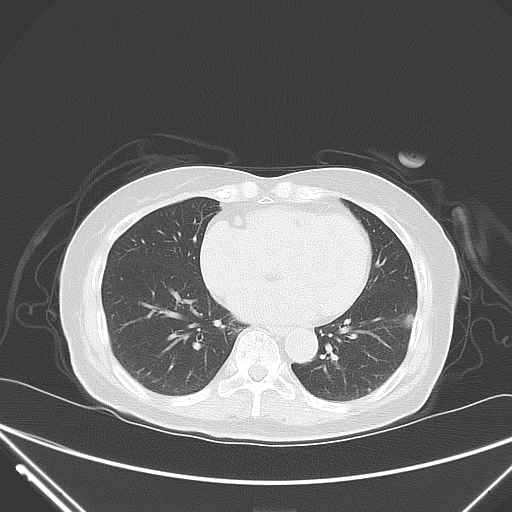
Chest CT, one axial slice; slice 24 of 62 in the series (ordered by position); 120 kVp; lung window (W 1500 / L -600 HU); 5 mm slice thickness; 512 × 512 image matrix, field of view 377 × 377 mm. Patient: female, 82 years. From the clinical record (not read from this slice): clinical TNM (as recorded): T1c N0 M0.
Structures marked on this image (bounding box drawn by a radiologist):
- lung tumour (recorded histology: adenocarcinoma): bounding box (x1, y1, x2, y2) in pixels: (396, 308, 418, 336)